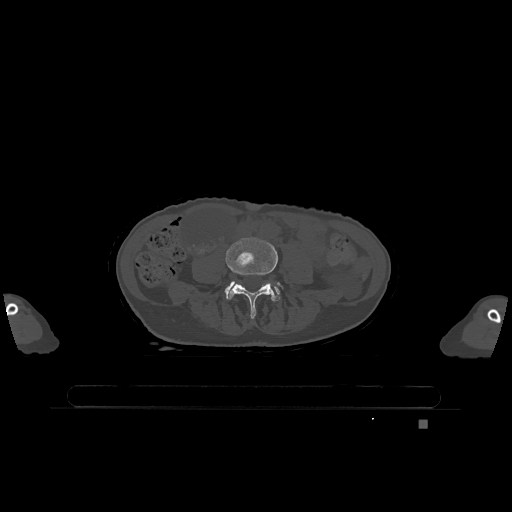
CT including the spine, one axial slice. Slice 289 of 1317 in the series (ordered by position). Bone window (W 1800 / L 400 HU). 512 × 512 image matrix, field of view 500 × 500 mm. Patient: female, 74 years. Case-level facts recorded for this patient, not image findings: primary cancer: lung; vertebrae with lytic lesions (as recorded): T1, T4, T5, T6, L4, L5.
Outlined on this slice (semi-automatic segmentation, software-assisted and operator-edited):
- L4 vertebra: box from (x=226, y=237) to (x=284, y=319) px
- L5 vertebra: (x=225, y=282)–(x=280, y=301)